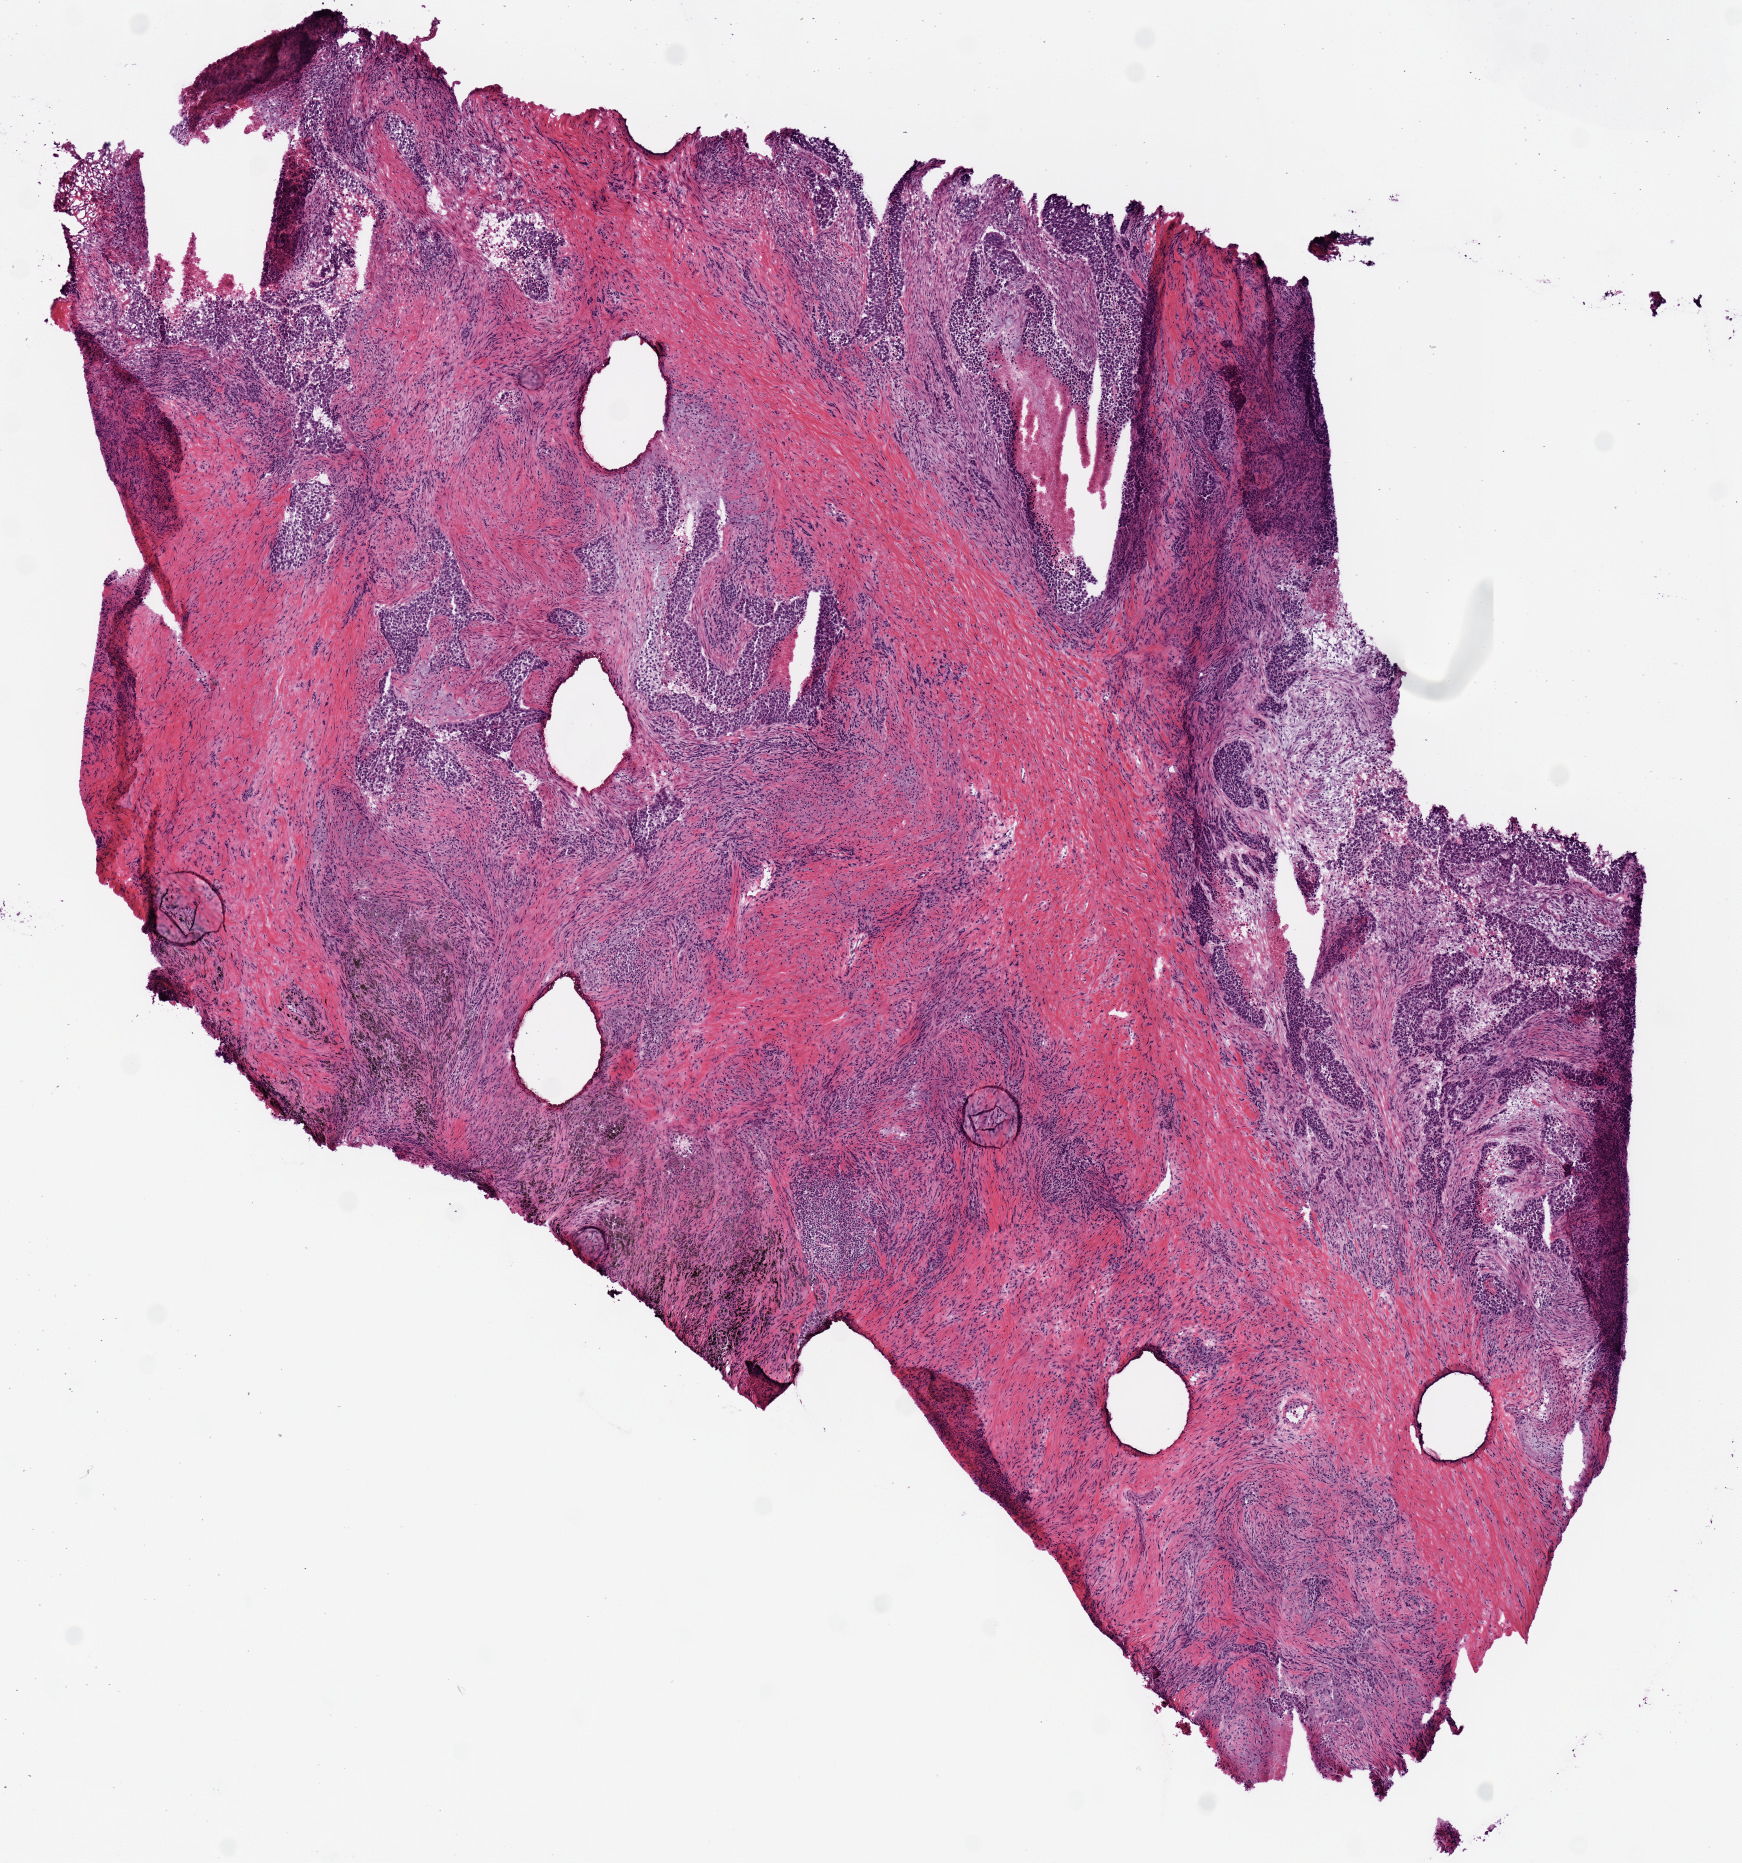
Digitized H&E tissue section (whole slide) — whole scanned area (about 6.9 x 7.4 mm, from a 20x scan) shown as a low-resolution overview; frozen section; primary tumour sample from the lung. Patient: male, age at initial diagnosis 68 years. Slide review estimates, as recorded: tumour cells 80%, tumour nuclei 65%, normal cells 0%, stromal cells 15%, necrosis 5%.
AJCC pathologic stage: IIIA (6th edition). Pathologic diagnosis: Squamous cell carcinoma, NOS.